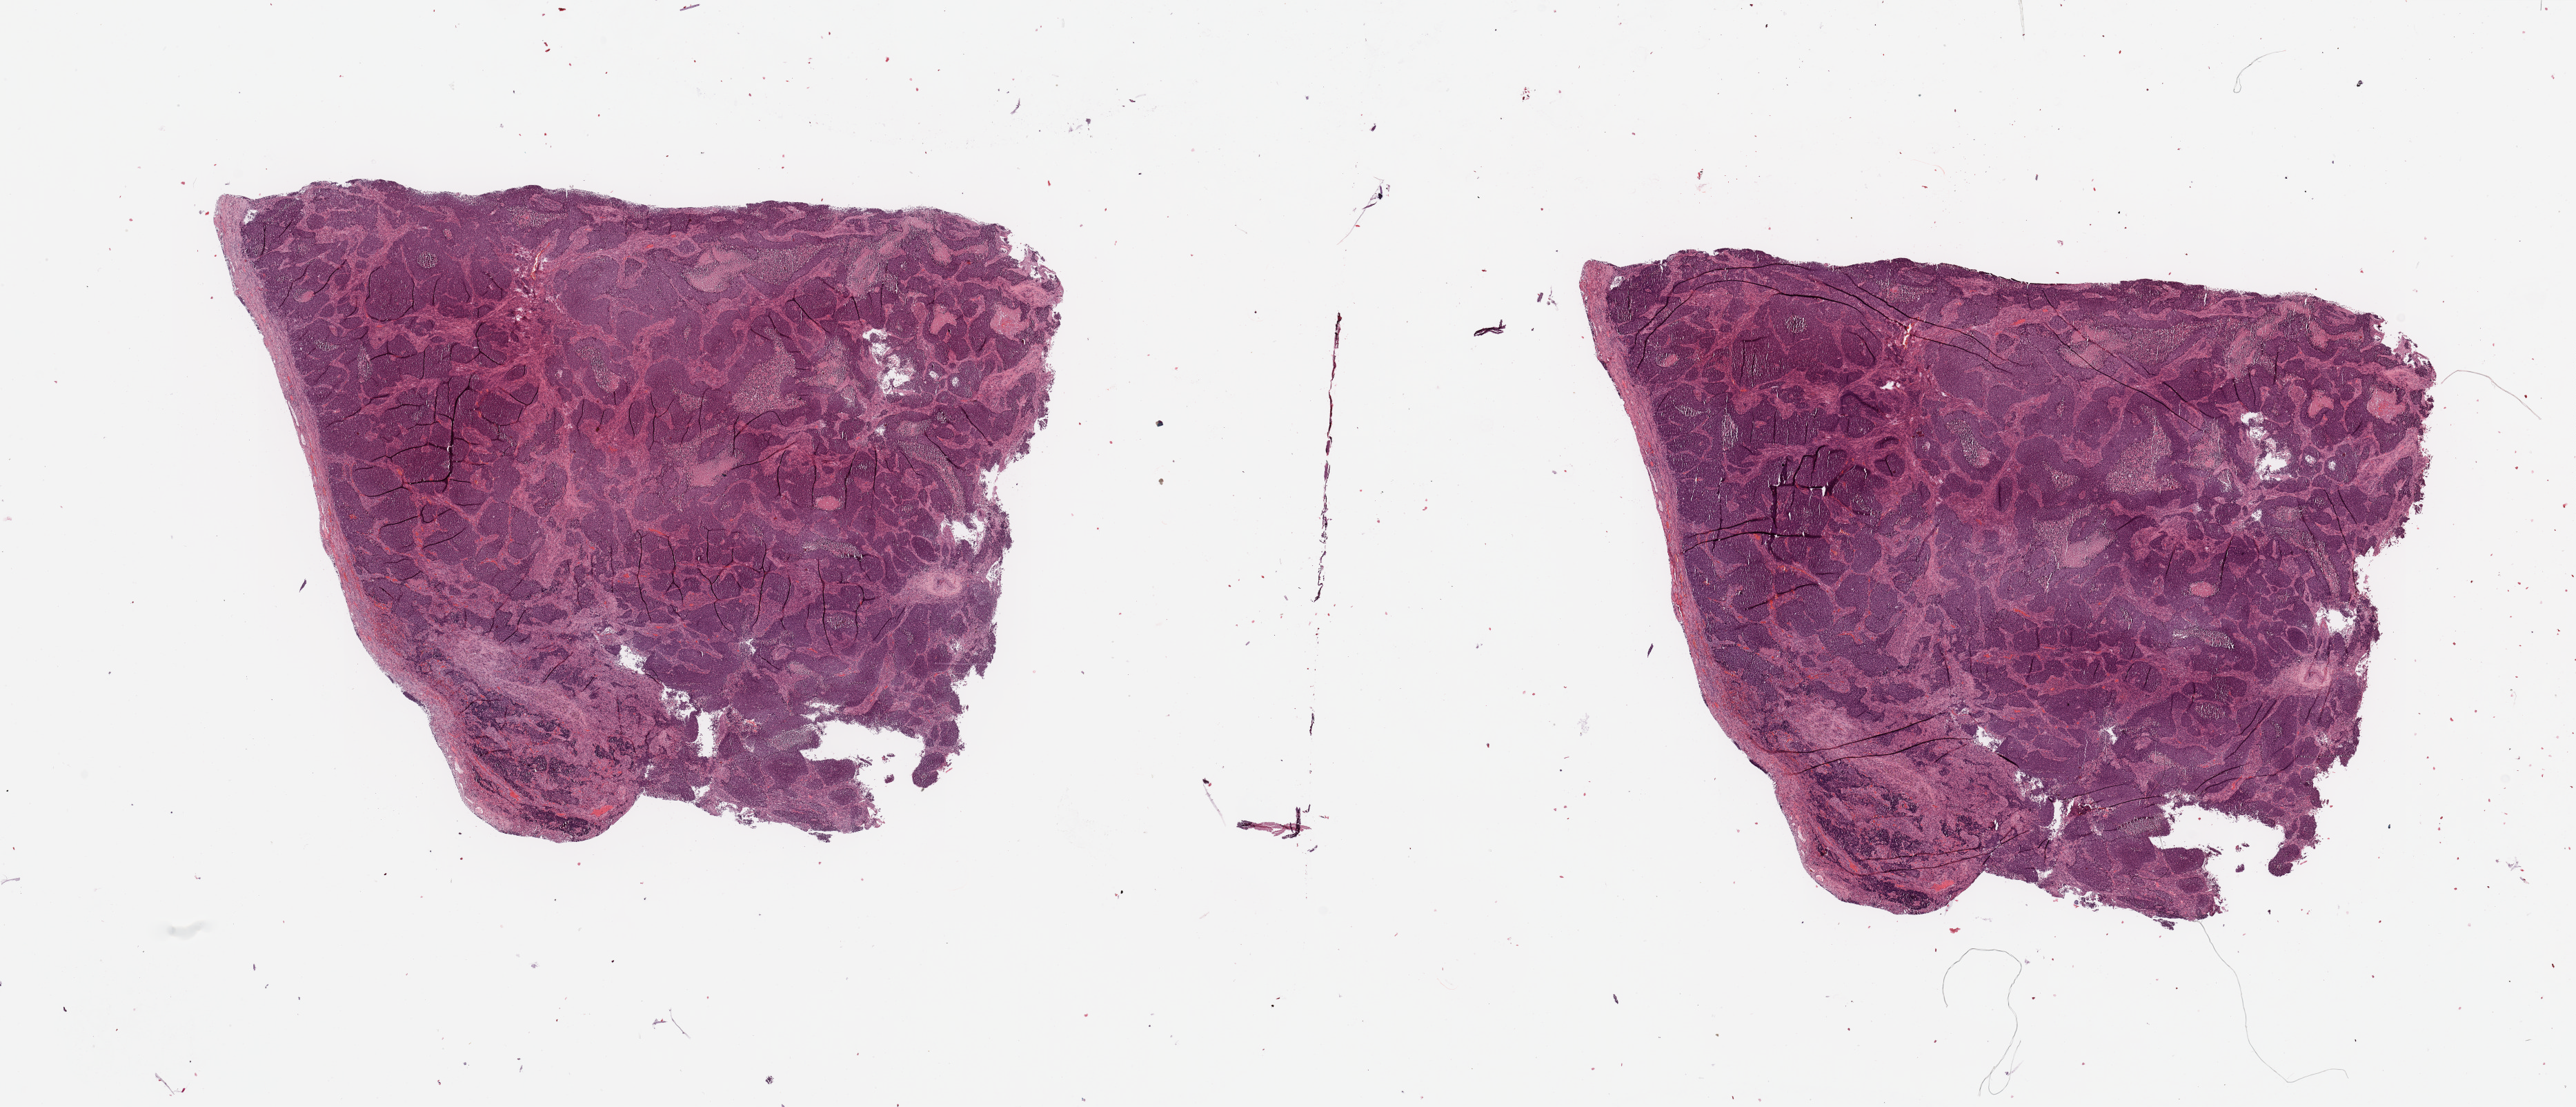
Digitized H&E-stained tissue section (whole slide), a low-resolution overview of the entire scanned area, about 29.5 x 12.7 mm (slide scanned at 20x), lung, tumour tissue. Patient: male, age 61 years. Histologic grade: G3 (poorly differentiated).
AJCC pathologic stage: IIB. Histologic diagnosis: Squamous cell carcinoma, NOS.